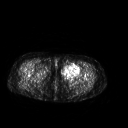
FDG PET of an extremity soft-tissue mass (from a PET/CT study), one axial slice; position 250 of 267 along the scan axis; 3.27 mm slice thickness; 128 × 128 image matrix, field of view 500 × 500 mm. Patient: female, 42 years. Case-level facts recorded for this patient, not image findings: histological type: pleiomorphic leiomyosarcoma; grade: intermediate; site of the primary tumour: left thigh.
Structures marked on this image (expert contour drawn on MRI and transferred to this co-registered scan by the dataset authors):
- gross tumour volume including surrounding oedema: bounding box (x1, y1, x2, y2) in pixels: (61, 63, 81, 80)
- gross tumour volume (mass): (61, 63, 81, 80)